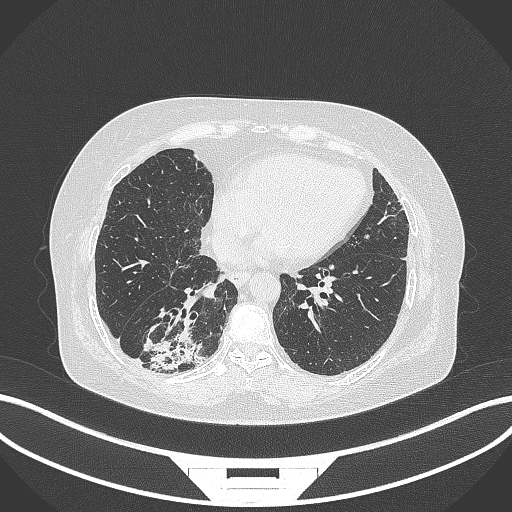
Chest CT, one axial slice; slice 77 of 296 in the series (ordered by position); lung window (W 1500 / L -600 HU); 512 × 512 image matrix, field of view 400 × 400 mm. Patient: female, 65 years. Case-level facts recorded for this patient, not image findings: clinical TNM (as recorded): T2b N1 M0; histopathological grade: G1.
Annotated regions visible in this slice (bounding box drawn by a radiologist):
- lung tumour (recorded histology: adenocarcinoma): bounding box [x1, y1, x2, y2] px = [138, 324, 205, 372]